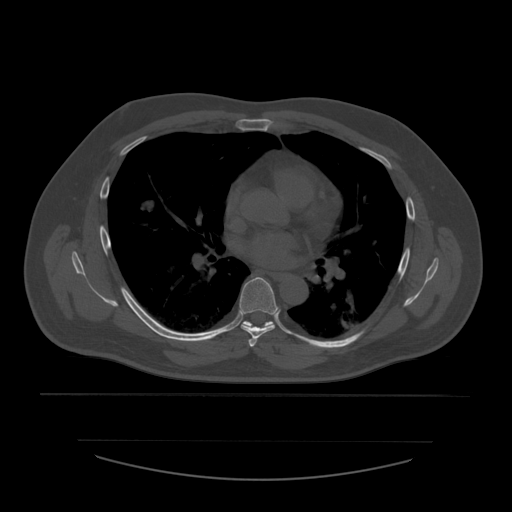
CT including the spine, one axial slice. Position 374 of 532 along the scan axis. Reconstruction kernel STANDARD. 120 kVp. Bone window (W 1800 / L 400 HU). 512 × 512 image matrix. Patient age 44 years. Case-level facts recorded for this patient, not image findings: primary cancer: soft tissue sarcoma.
Outlined on this slice (semi-automatic segmentation, software-assisted and operator-edited):
- T5 vertebra: box from (x=249, y=338) to (x=258, y=347) px
- T6 vertebra: (x=240, y=278)–(x=279, y=340)
- T7 vertebra: (x=243, y=321)–(x=273, y=327)